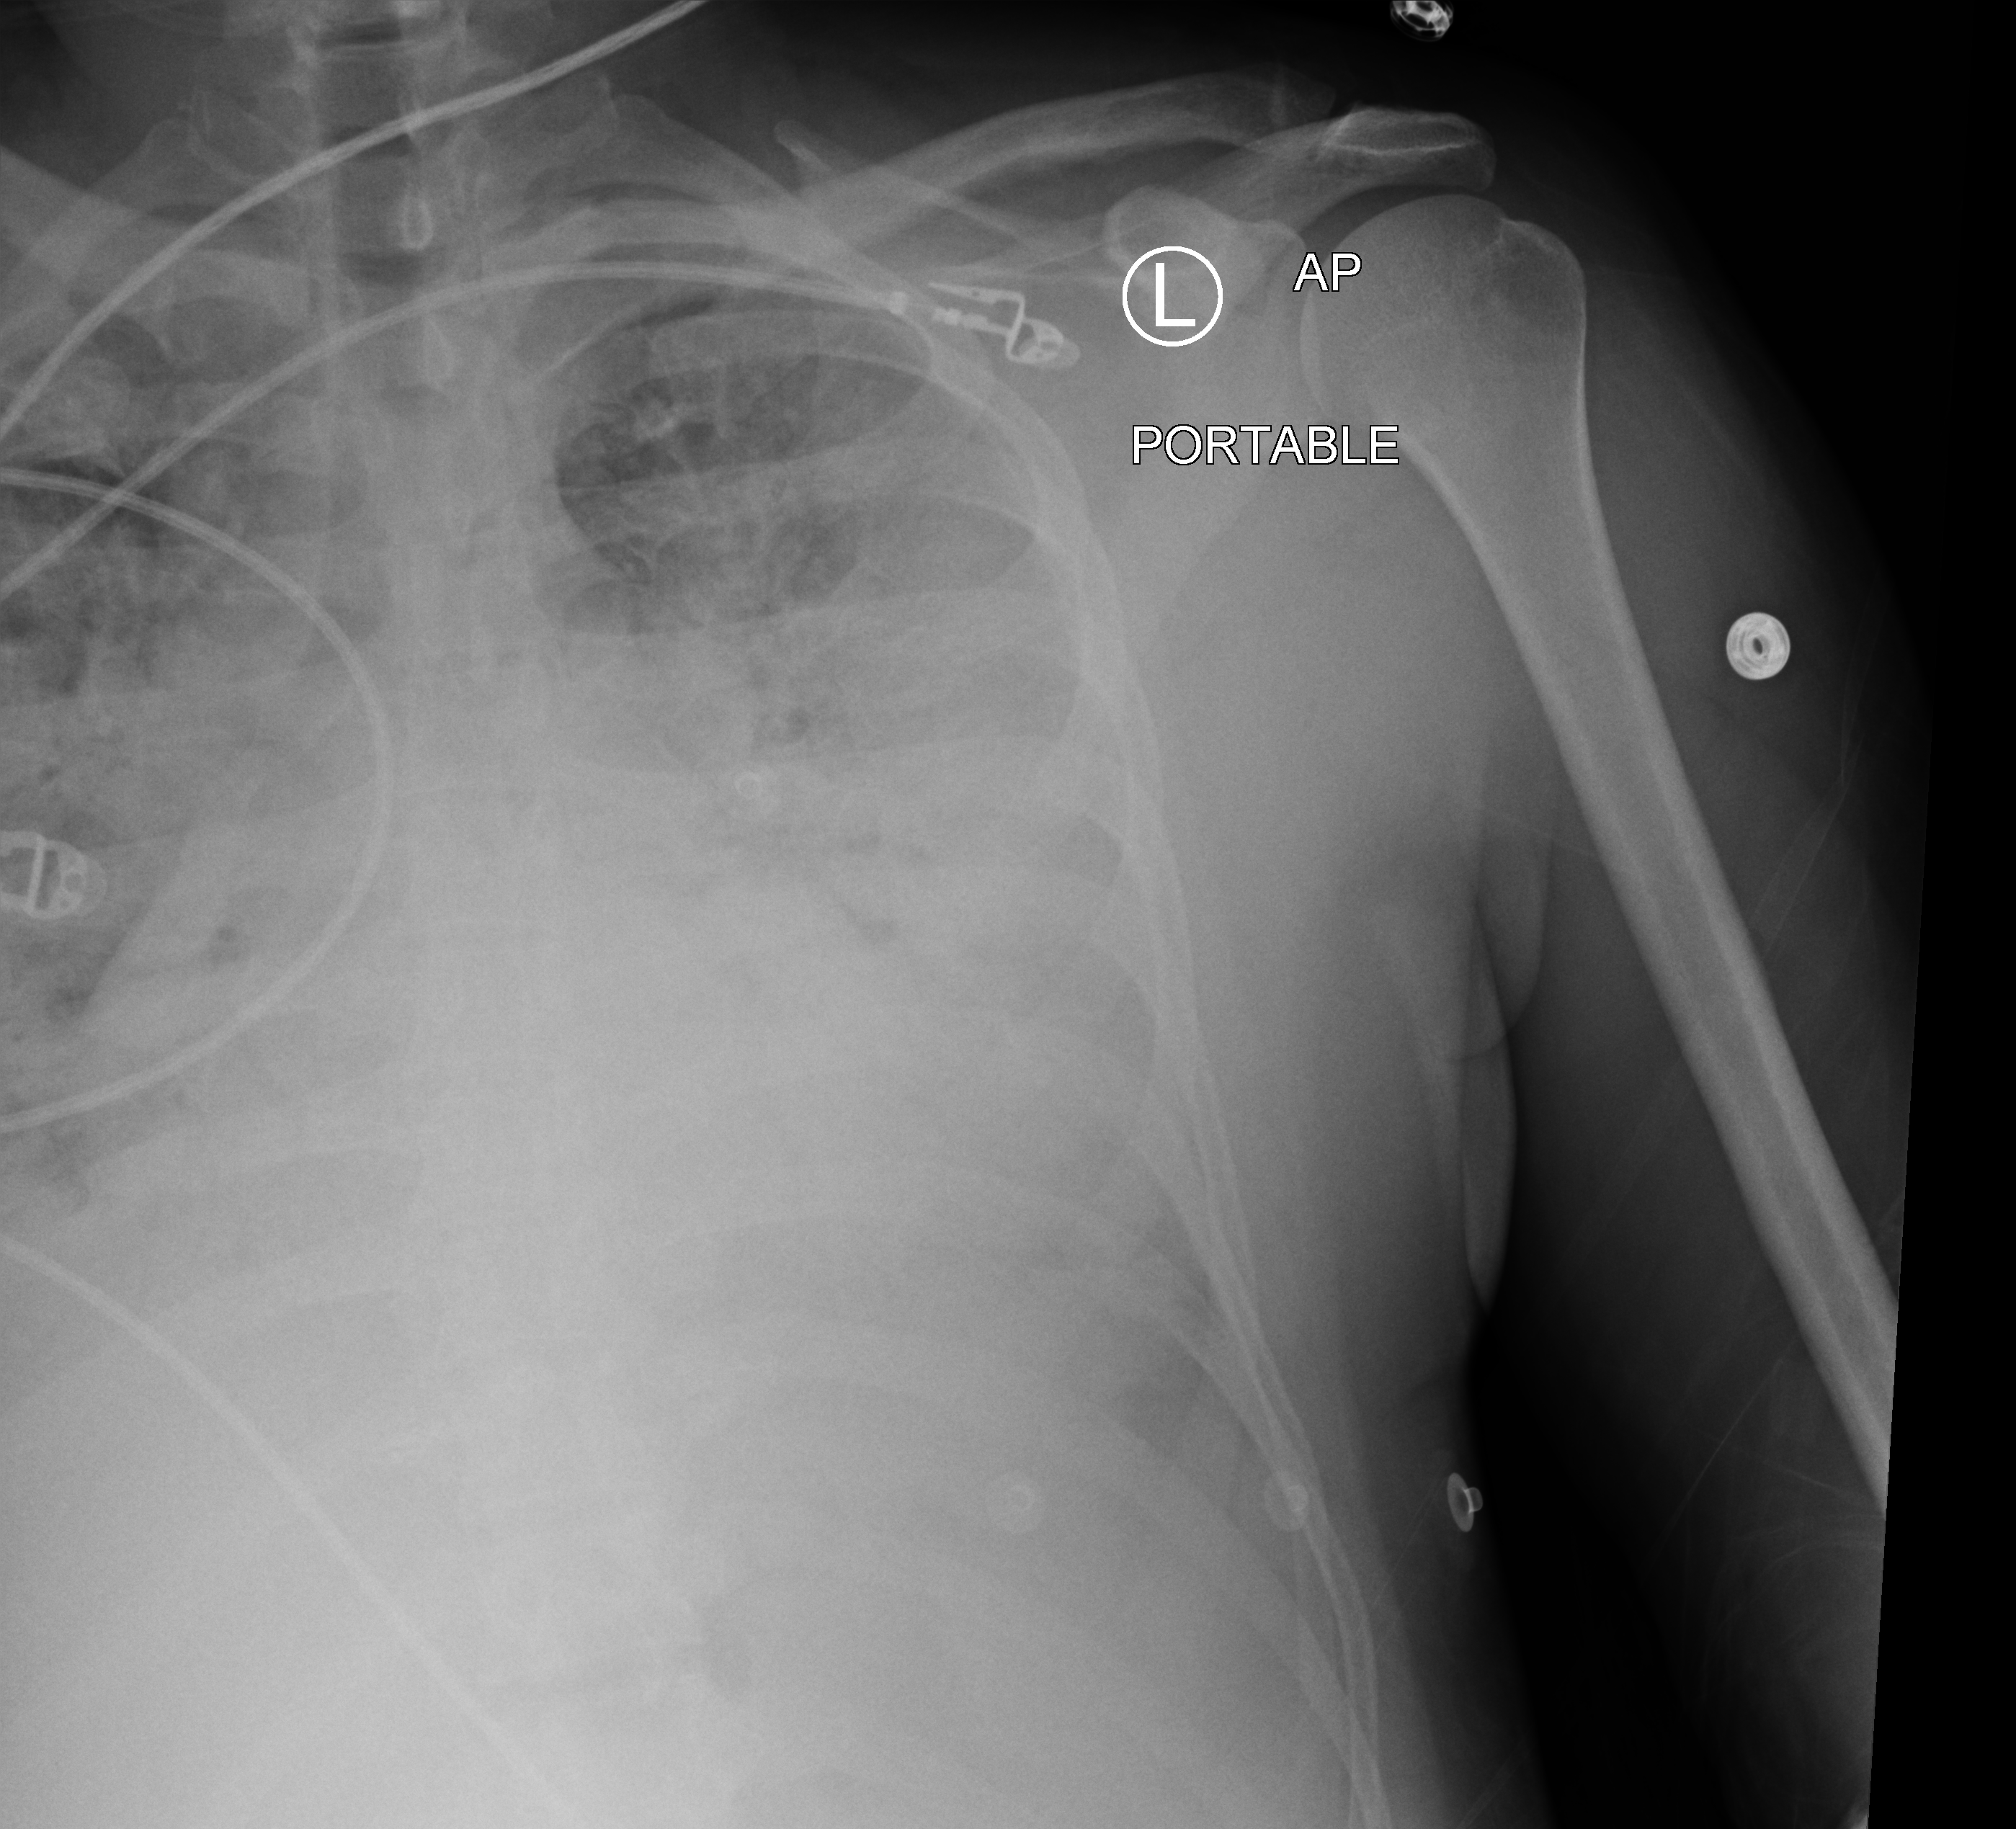
Portable chest radiograph; anteroposterior (AP) projection. Male patient hospitalised with COVID-19, age 18–59 years.
Admission-level facts for this patient (not findings on this image; timing relative to this image not recorded): mechanically ventilated during this hospital stay: yes.